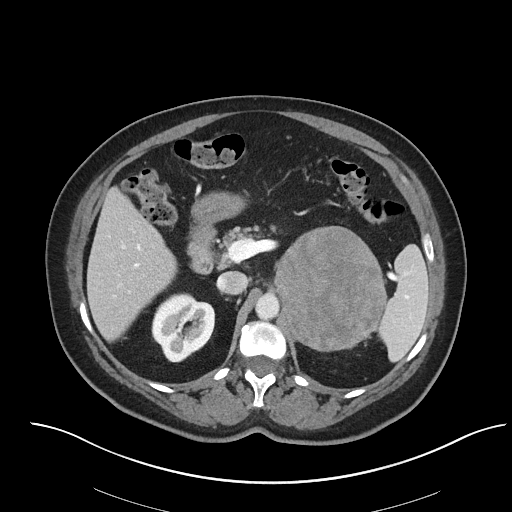
Contrast-enhanced abdominal CT, one axial slice. Slice 47 of 92 in the series (ordered by position). Intravenous contrast given. Soft-tissue window (W 400 / L 40 HU). 3 mm slice thickness. 512 × 512 image matrix, field of view 440 × 440 mm. Patient: female, 53 years. Case-level facts recorded for this patient, not image findings: diagnosis: adrenocortical carcinoma; tumour side: left adrenal; tumour size at pathology: 9 cm; Ki-67 index: 28 %; stage (as recorded): 2.
Annotated regions visible in this slice (semi-automatically segmented with operator editing):
- mass: bounding box (x1, y1, x2, y2) in pixels: (276, 227, 385, 350)